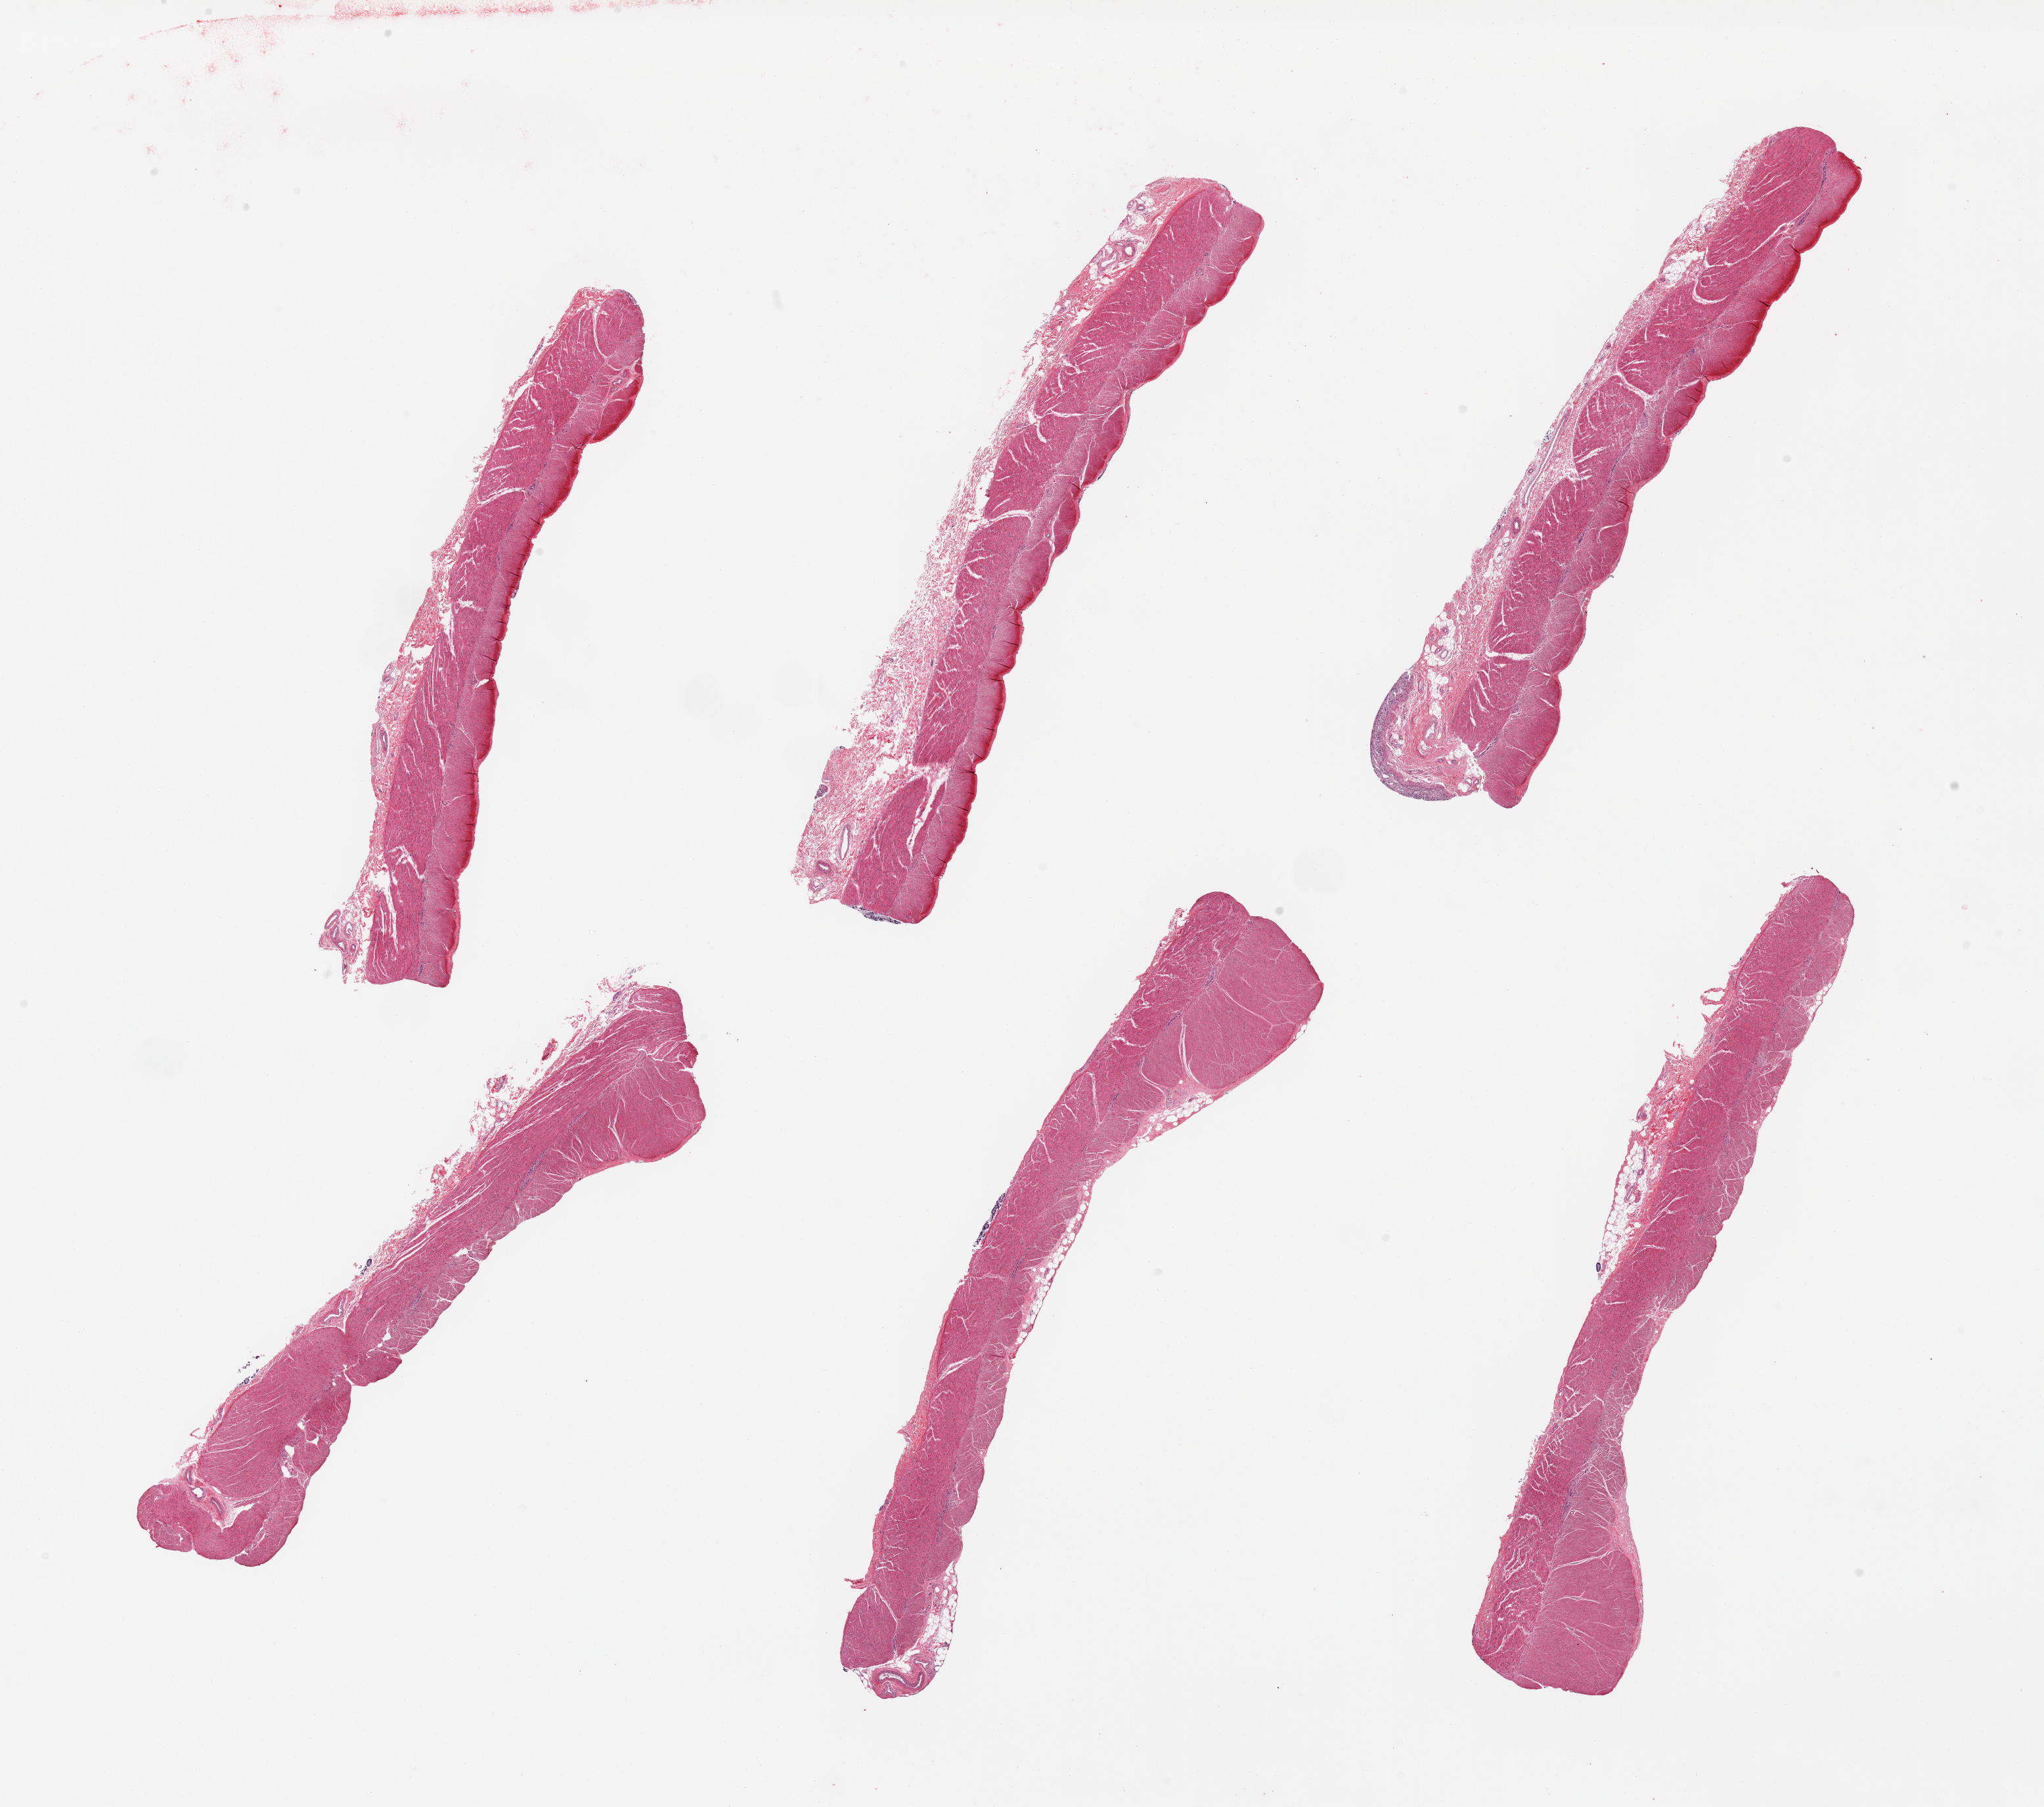
Whole-slide image, hematoxylin and eosin (H&E) stain — a low-resolution overview of the entire scanned area, about 24.6 x 21.8 mm. PAXgene-fixed, paraffin-embedded tissue. Section of sigmoid colon (target tissue). Donor tissue sample. Donor: female.
Review note (as recorded): 6 pieces, confirmed target muscularis, trace degenerated lamina propria on section.